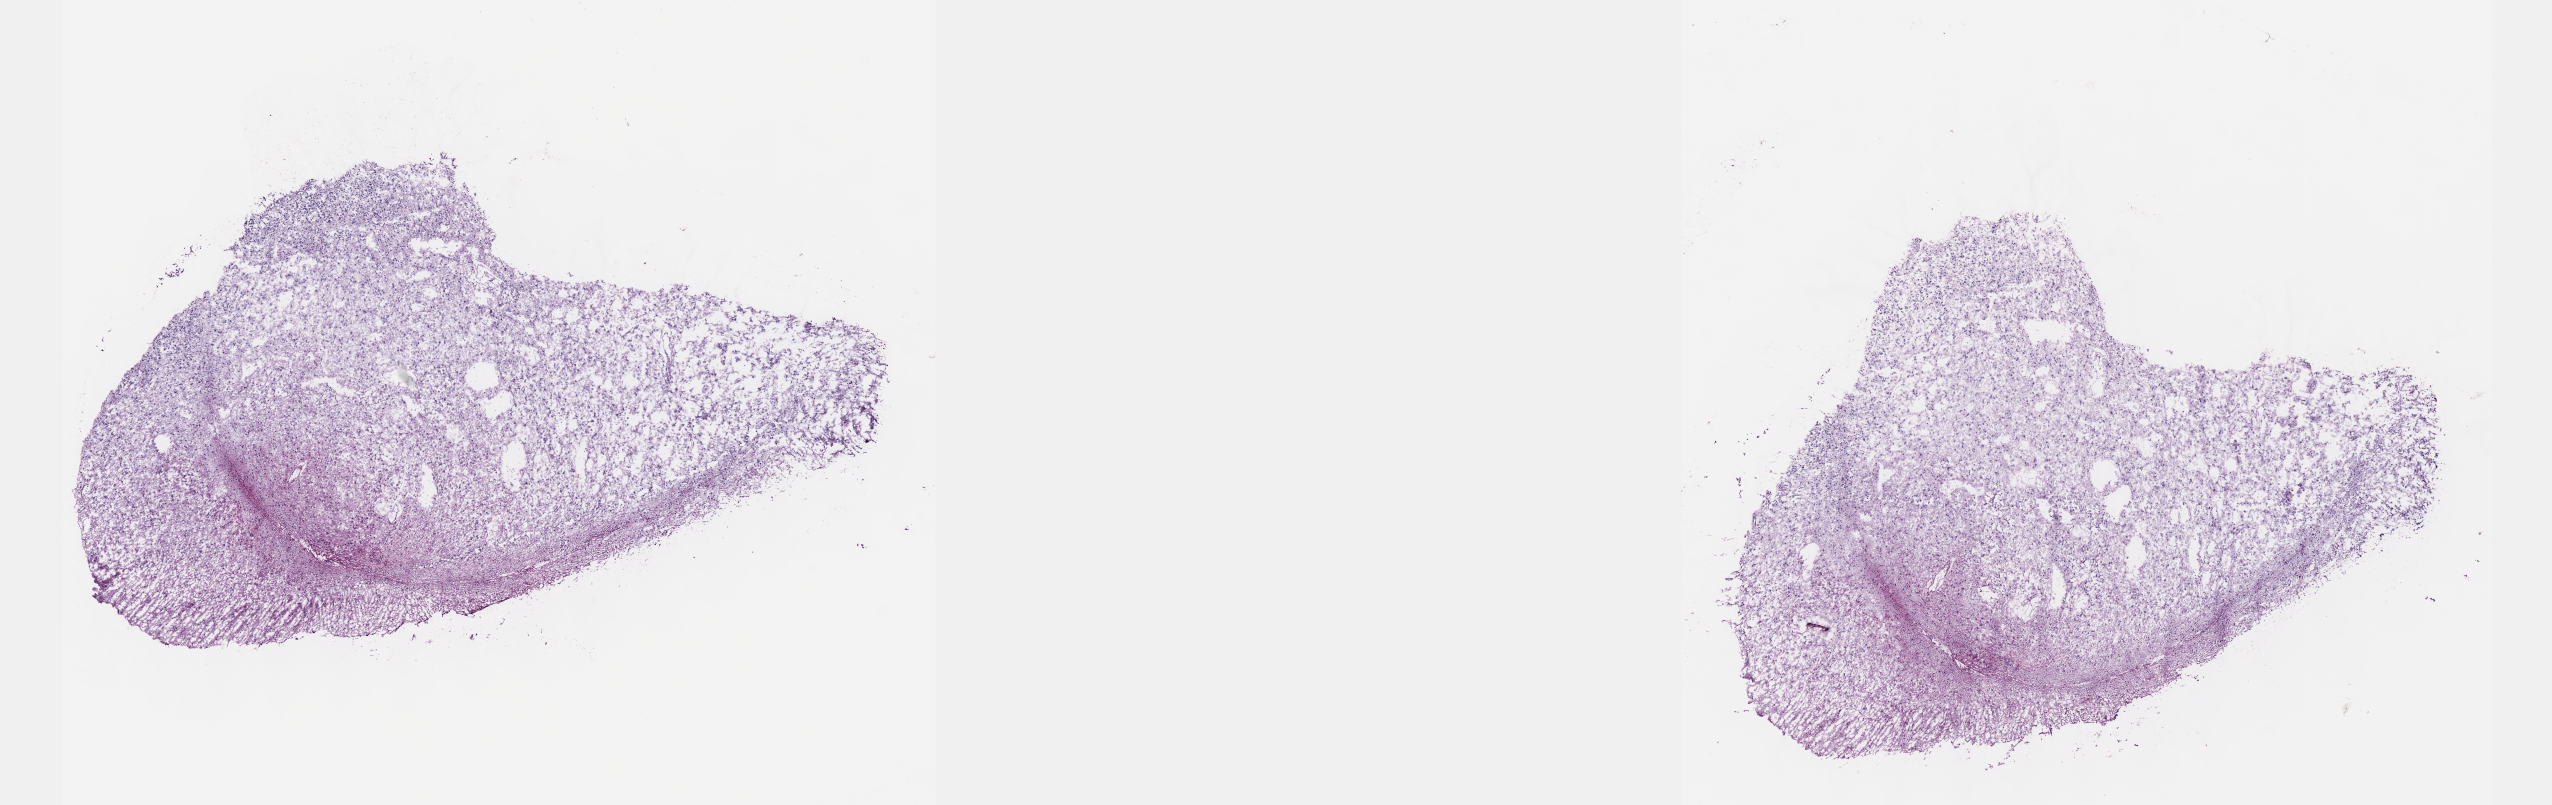
Whole-slide histology image, H&E-stained — a low-resolution overview of the entire scanned area, about 20.6 x 6.5 mm (slide scanned at 40x); frozen section from the top of the tissue portion; primary tumour sample from the brain. Female, age 25 years at initial diagnosis. Histologic grade: G2 (moderately differentiated). Pathologist review of this section (percent, as recorded): tumour cells 40%, tumour nuclei 90%, normal cells 10%, stromal cells 50%, necrosis 0%. Infiltration values recorded for this section: lymphocyte infiltration 0%, monocyte infiltration 0%, neutrophil infiltration 0%.
Histologic diagnosis: Mixed glioma (cerebrum). Laterality: left.